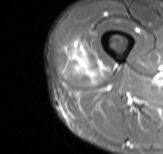
MRI of an extremity soft-tissue mass, one axial slice; position 16 of 61 along the scan axis; STIR; MR volume resampled by the dataset authors to the PET/CT grid (not the native acquisition matrix); 3.27 mm slice thickness; 163 × 154 image matrix. Male patient. Case-level facts recorded for this patient, not image findings: histological type: poorly differentiated synovial sarcoma; grade: high; site of the primary tumour: right buttock.
Structures marked on this image (expert contour drawn on MRI and transferred to this co-registered scan by the dataset authors):
- gross tumour volume including surrounding oedema: box from (x=66, y=41) to (x=104, y=77) px